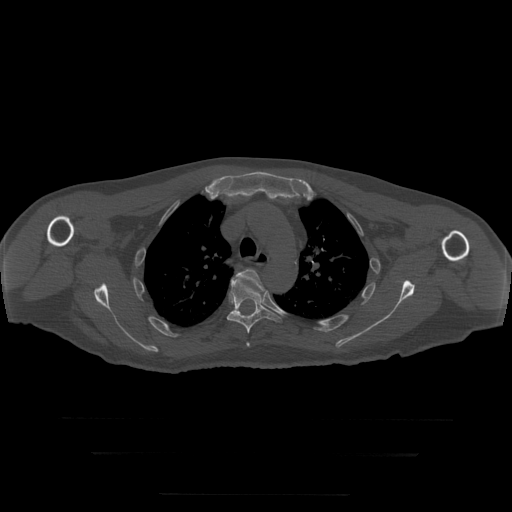
CT including the spine, one axial slice. Slice 228 of 397 in the series (ordered by position). Bone window (W 1800 / L 400 HU). 1.25 mm slice thickness. 512 × 512 image matrix, field of view 510 × 510 mm. Patient age 73 years. From the clinical record (not read from this slice): primary cancer: prostate.
Outlined on this slice (semi-automatic segmentation, software-assisted and operator-edited):
- T4 vertebra: bounding box <237,270,266,347> (left, top, right, bottom; pixels)
- T5 vertebra: <227,276,283,346>
- T6 vertebra: <232,310,240,315>